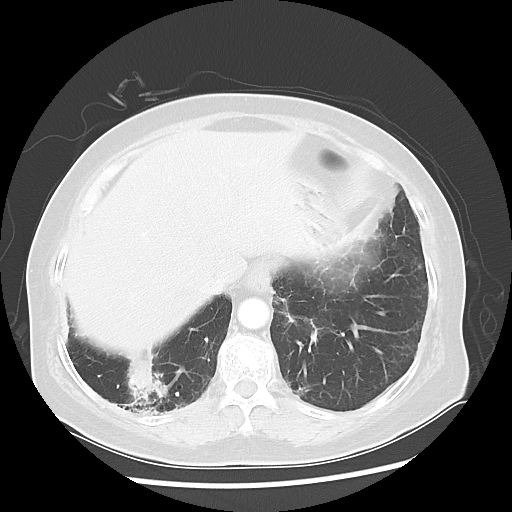
Chest CT, one axial slice; position 13 of 56 along the scan axis; lung window (W 1500 / L -600 HU); 5 mm slice thickness; 512 × 512 image matrix. Female patient, age 64 years. Case-level facts recorded for this patient, not image findings: clinical TNM (as recorded): Tis N0 M0.
Structures marked on this image (rectangle marked by the reading radiologist):
- lung tumour (recorded histology: adenocarcinoma): bounding box <117,346,175,420> (left, top, right, bottom; pixels)